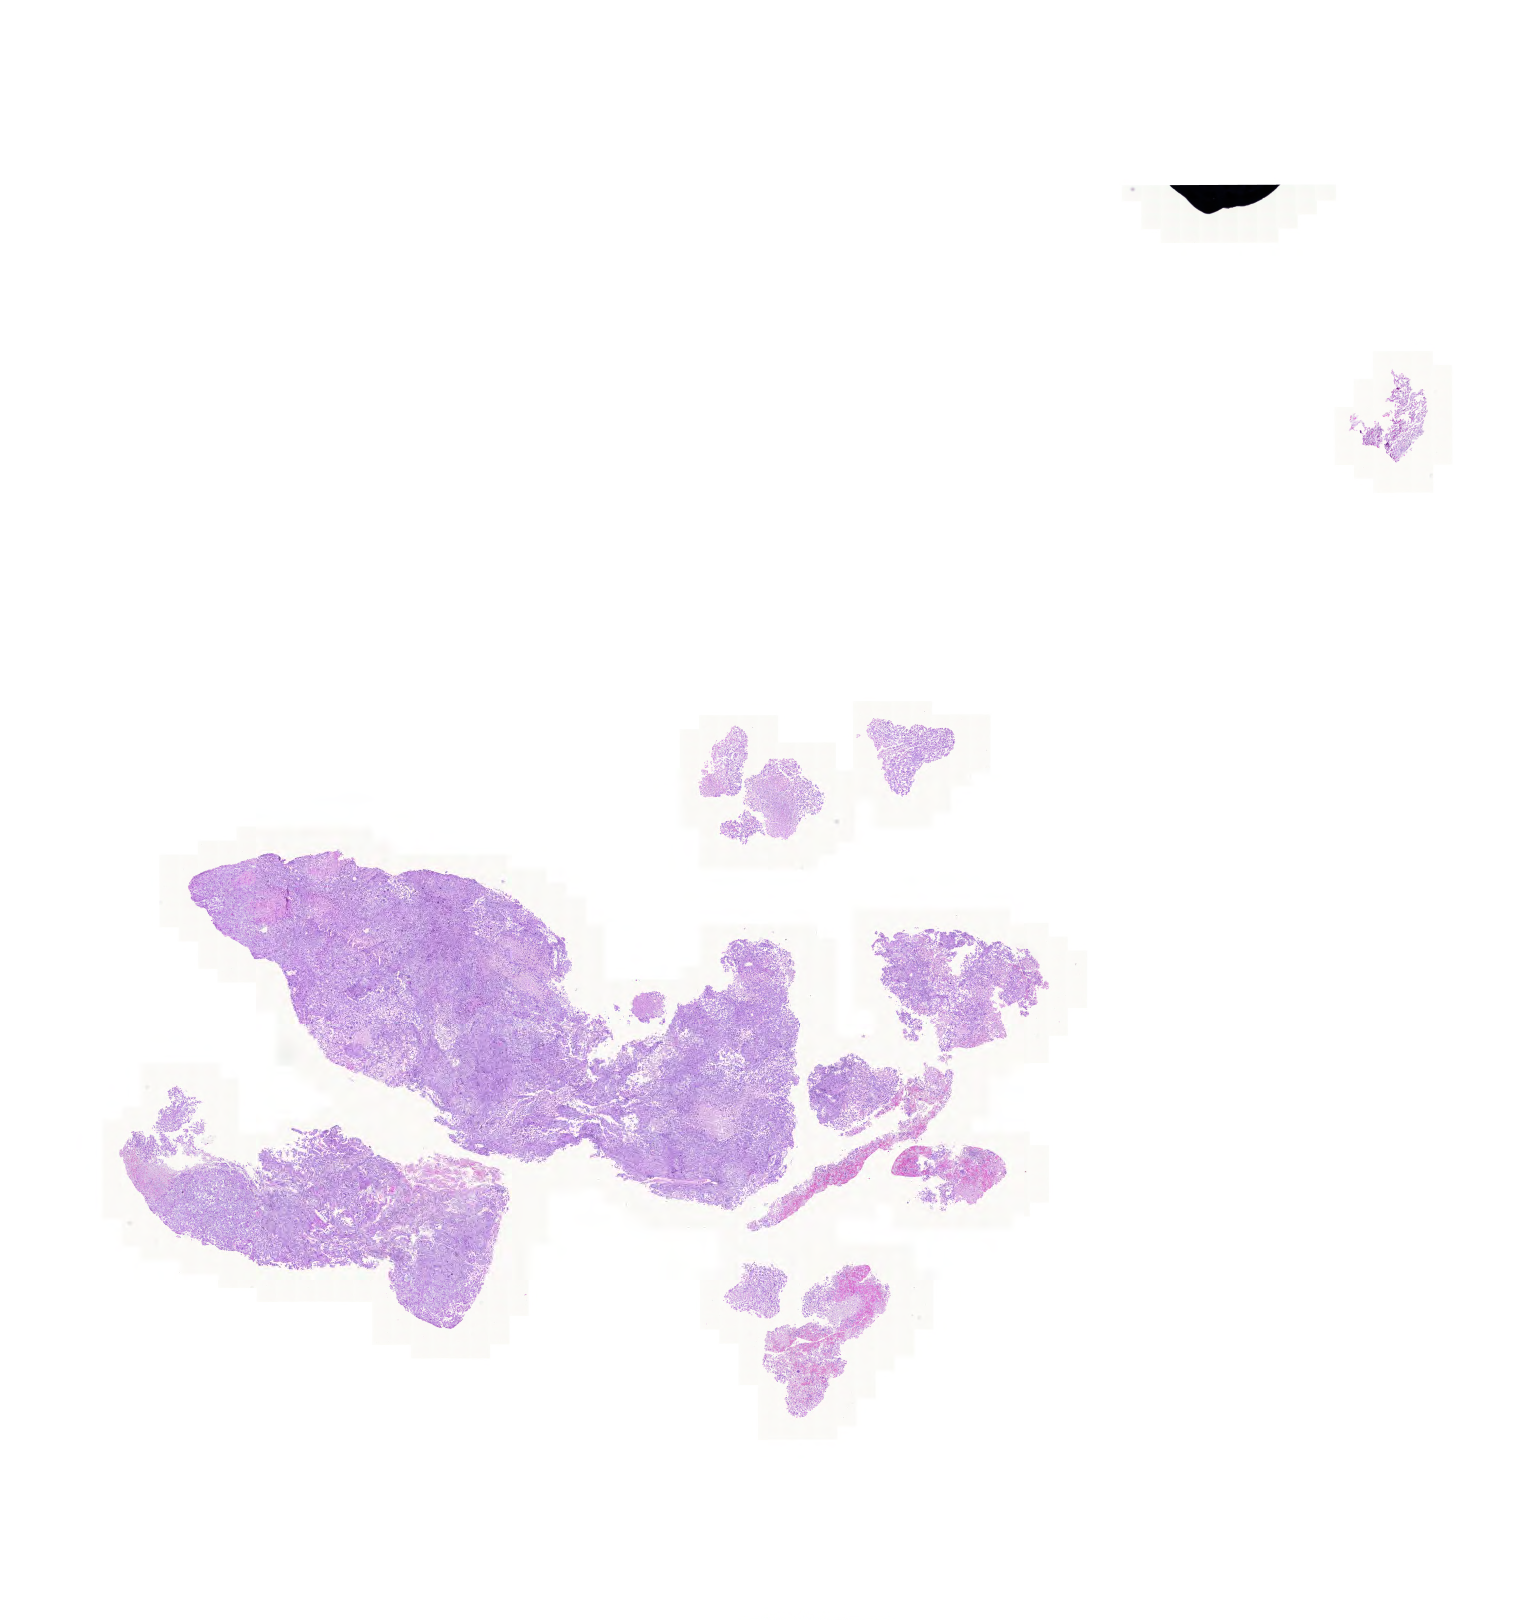
Whole-slide histology image, H&E — a low-resolution overview of the entire scanned area, about 22.9 x 24.1 mm (acquisition: 20x scan), formalin-fixed paraffin-embedded (FFPE) diagnostic section, lung, primary tumour sample. Patient: male, age at initial diagnosis 57 years.
Histologic diagnosis: Adenocarcinoma with mixed subtypes (lower lobe, lung).